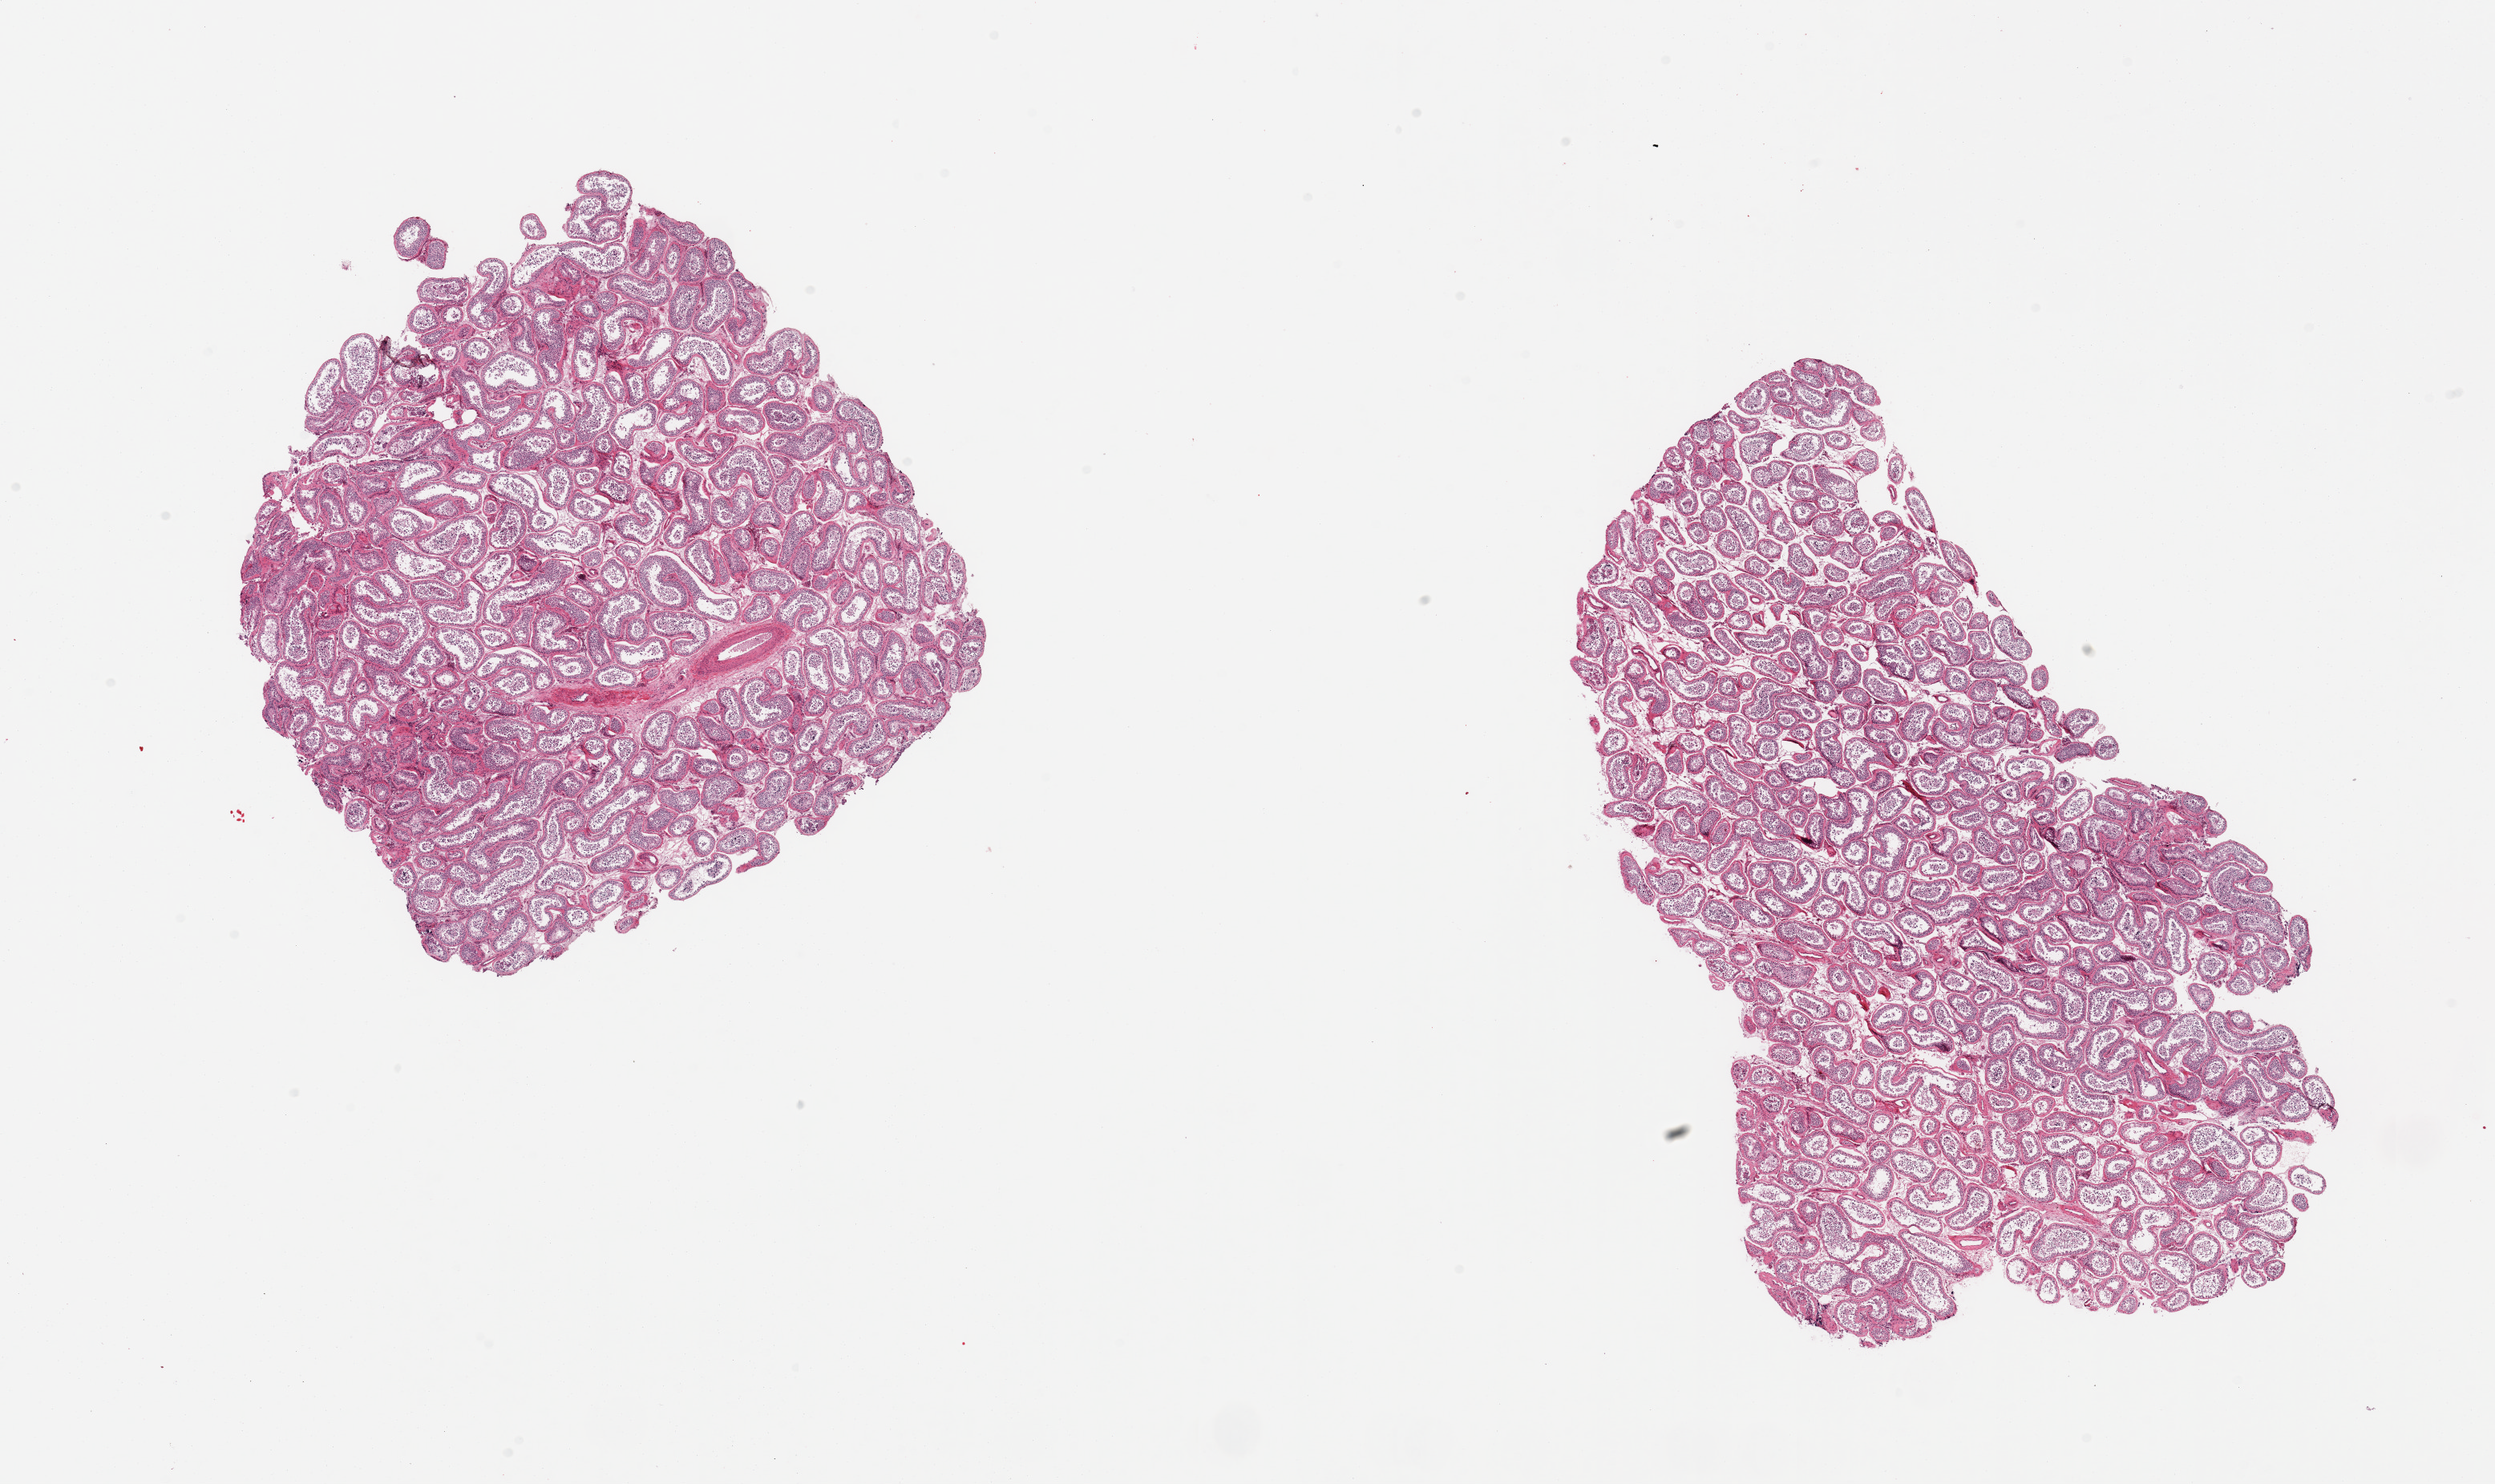
H&E whole-slide image, shown as a low-resolution overview of the whole scanned area (about 24.6 x 14.6 mm); PAXgene-fixed paraffin-embedded (PFPE) section; sampled site (target tissue): testis; donor tissue sample. Donor: male.
Reviewer comment on this tissue sample: 2 pieces; spermatogenesis is present.